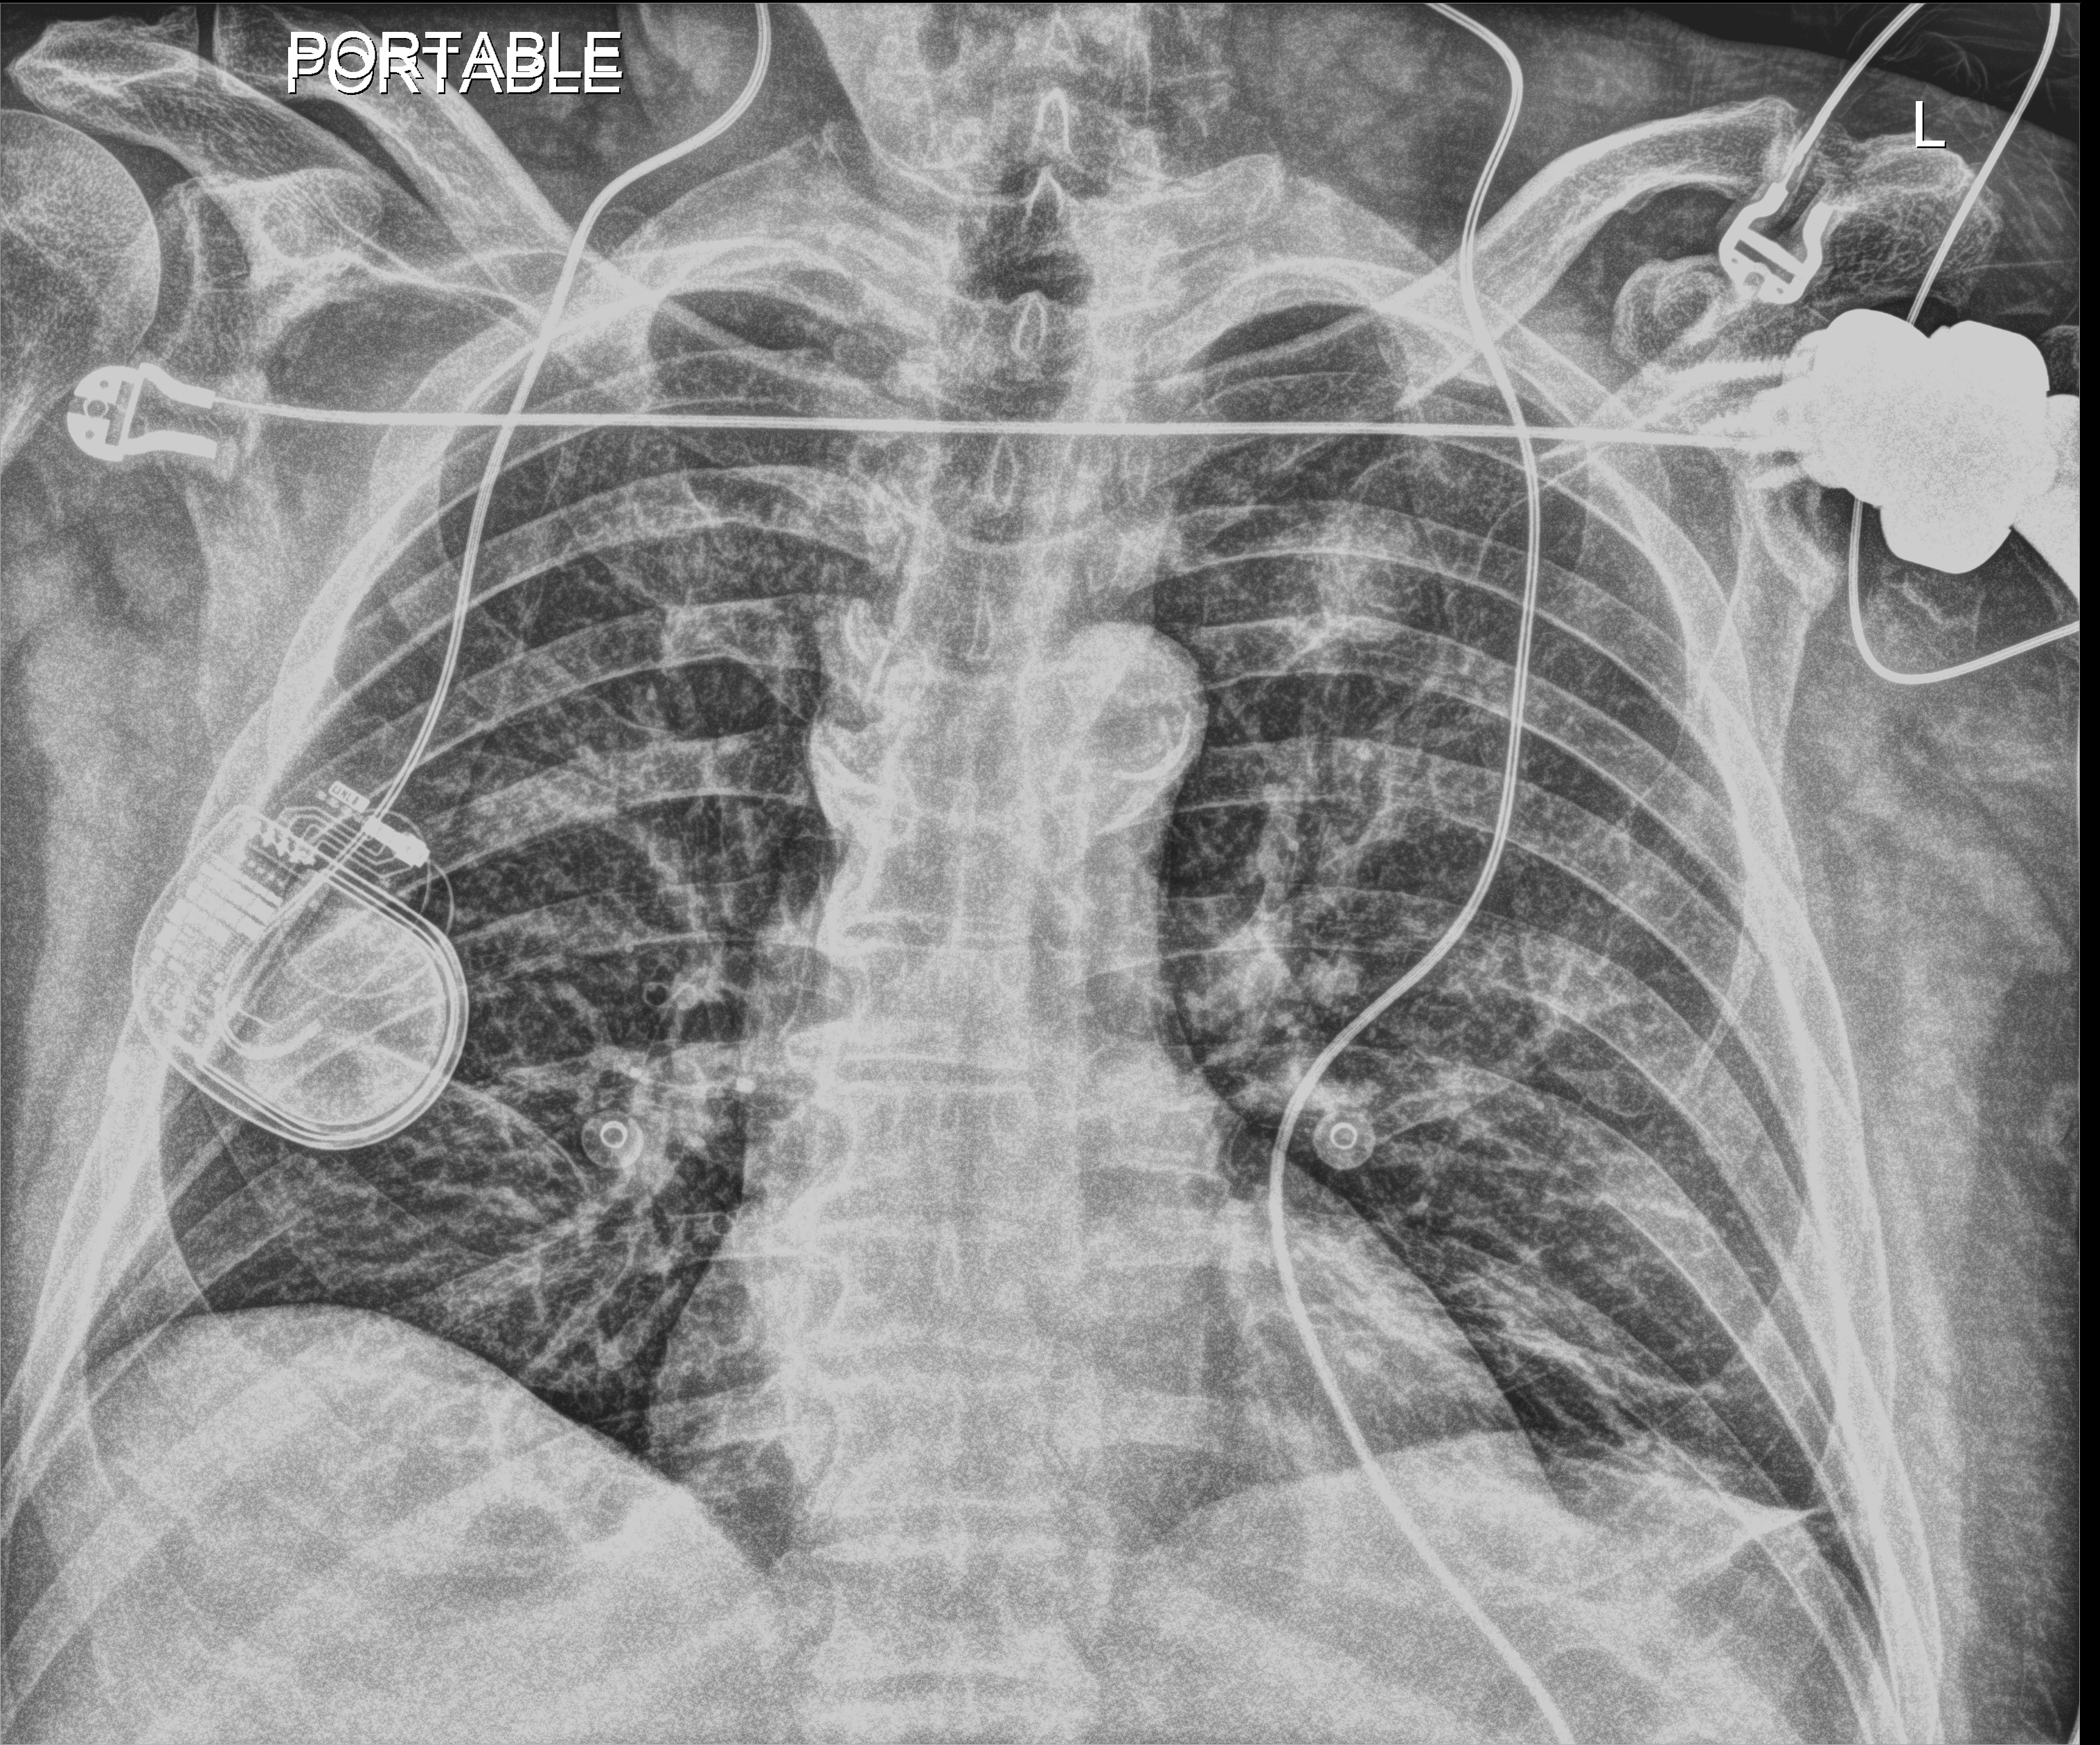
Portable chest radiograph; anteroposterior (AP) projection. Patient hospitalised with COVID-19; male, aged 60–74 years.
Admission-level facts for this patient (not findings on this image; timing relative to this image not recorded): admitted to intensive care during this hospital stay: no.